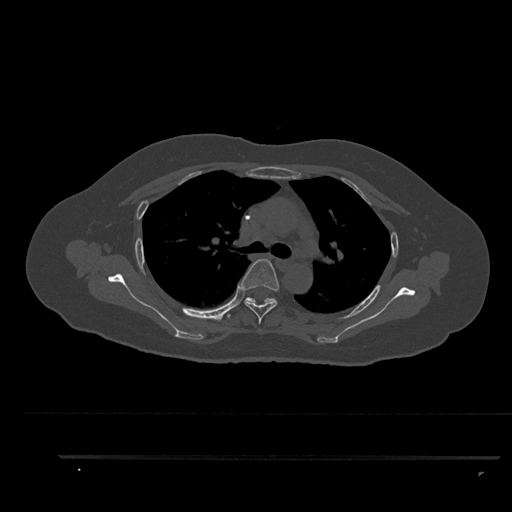
CT including the spine, one axial slice; 120 kVp; bone window (W 1800 / L 400 HU); 0.5 mm slice thickness; 512 × 512 image matrix, field of view 408 × 408 mm. Patient: female, 44 years. Case-level facts recorded for this patient, not image findings: primary cancer: renal.
Annotated regions visible in this slice (semi-automatic segmentation, software-assisted and operator-edited):
- T4 vertebra: bounding box [x1, y1, x2, y2] px = [240, 259, 279, 324]
- T5 vertebra: [227, 297, 273, 318]